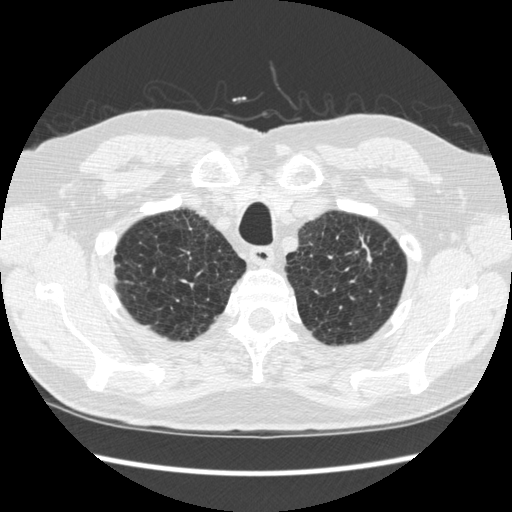
Chest CT (low-dose screening protocol), one axial image; second annual screen; lung window (W 1500 / L -600 HU); standard (soft-tissue) reconstruction kernel (STANDARD); slice 41 of 295 in the series. Male participant, aged 70 years at enrolment.
Expert reader's lesion annotation, bounding box [x1, y1, x2, y2] px = [329, 224, 391, 292]. The screening reader recorded 5 non-calcified nodules or masses ≥4 mm on this exam (right lower lobe, right lower lobe, right lower lobe, left upper lobe, left lower lobe); which of them this box marks is not recorded. Official screen result: positive, change unspecified: nodule(s) >= 4 mm or enlarging nodule(s), mass(es), or other non-specific abnormalities suspicious for lung cancer. Later outcome: lung cancer diagnosed 479 days after this screen (after the third annual screen) — squamous cell carcinoma, NOS, left upper lobe, moderately differentiated (G2), stage IA (AJCC 6th edition), 18 mm at pathology.